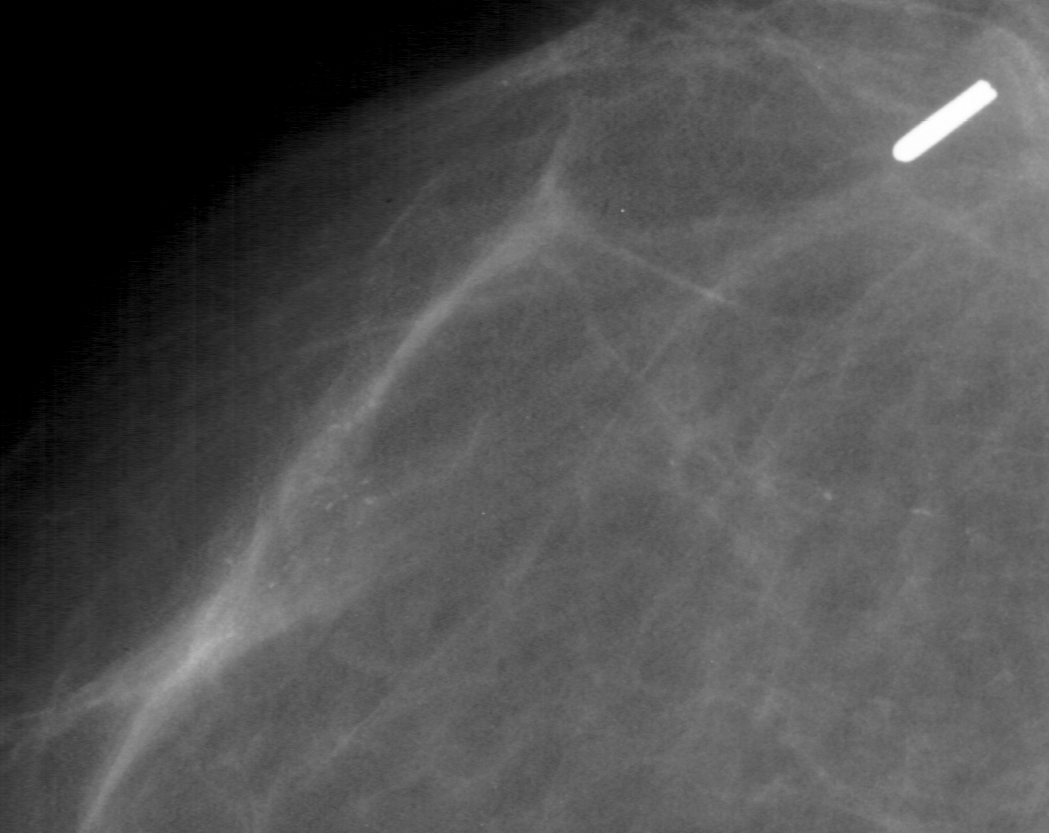
Crop from a digitized film mammogram around one marked abnormality, left breast, CC view, BI-RADS breast density category 3 (scale 1–4).
Finding: calcifications, morphology pleomorphic, distribution linear; BI-RADS assessment category 5; subtlety rating 4 on a 1 (subtle) to 5 (obvious) scale; pathology result (as recorded, not read from the image): malignant.